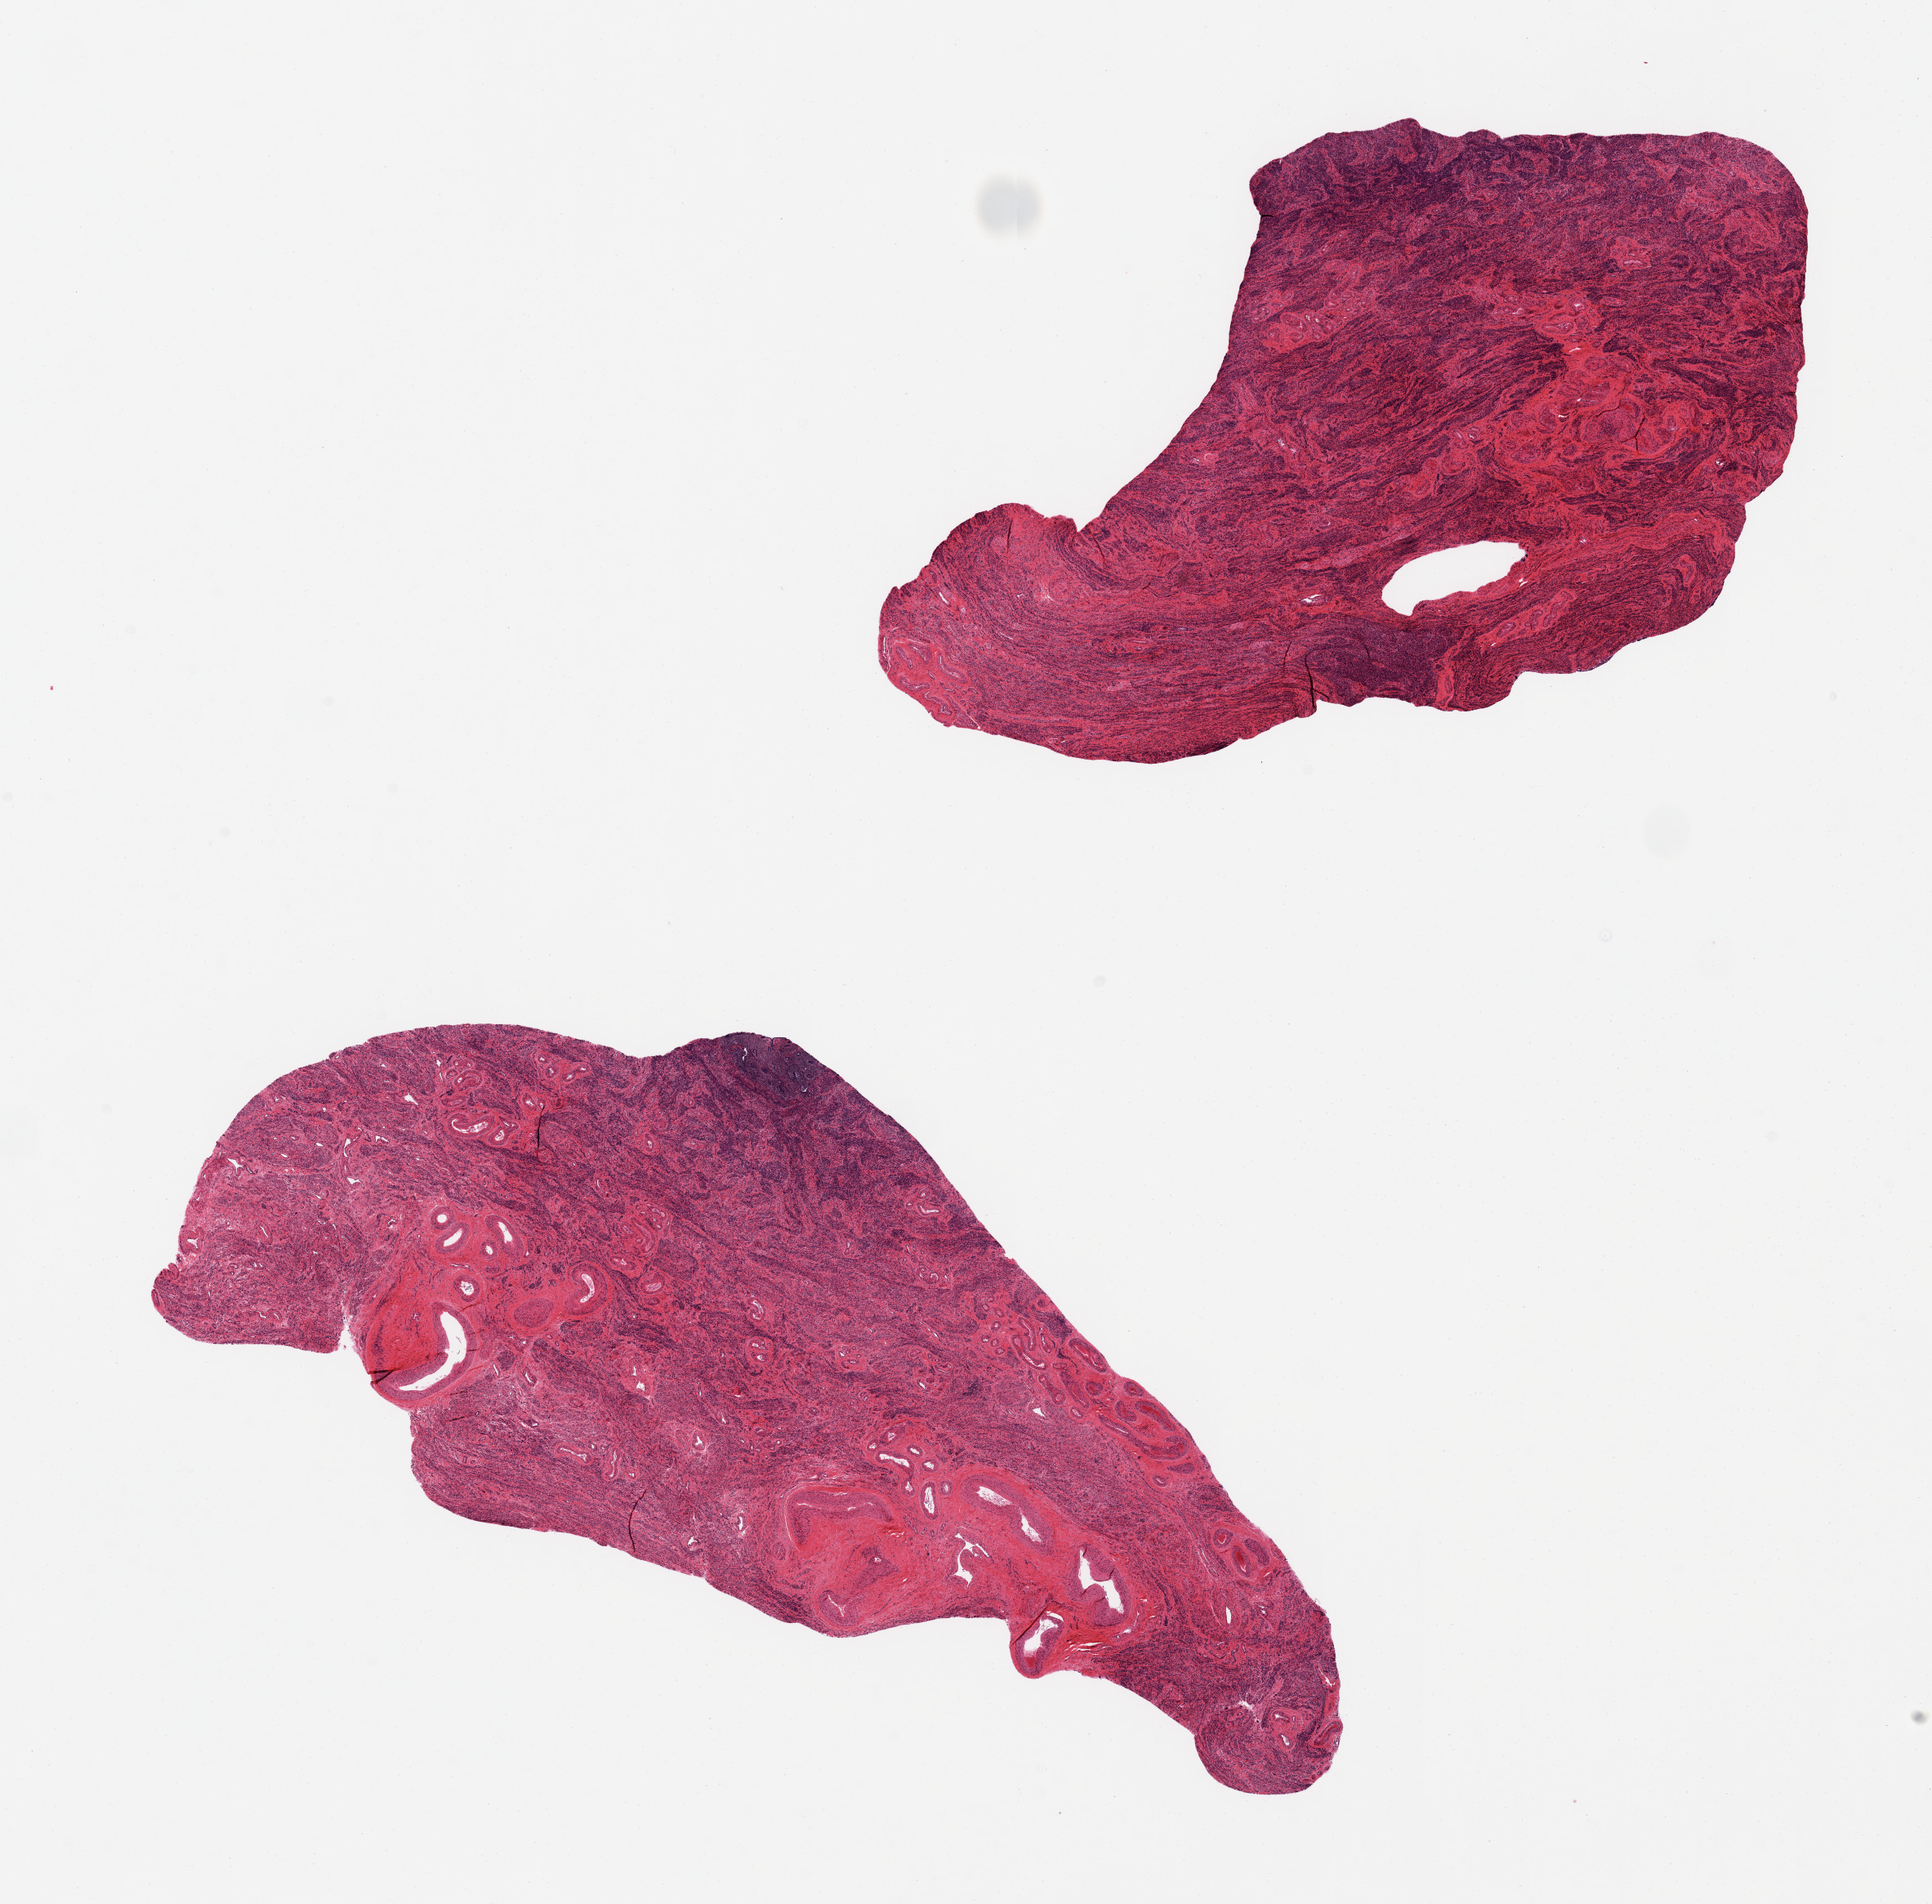
Digitized H&E-stained section — whole scanned area (about 18.7 x 18.4 mm, from a 20x scan) shown as a low-resolution overview. PAXgene-fixed, paraffin-embedded tissue. Sampled site (target tissue): uterus. Donor tissue sample. Female donor.
Review note (as recorded): 2 pieces; small focus of endometrium present.